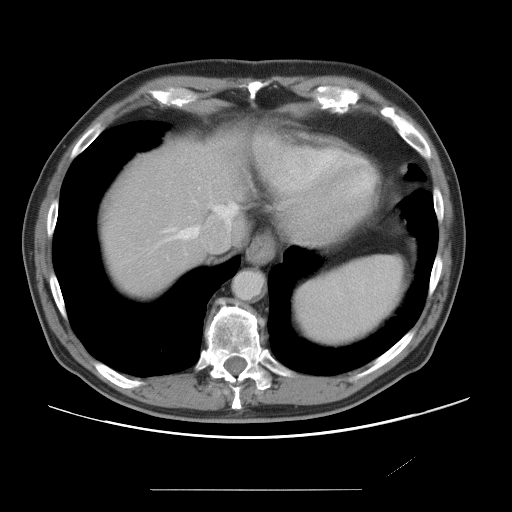
Contrast-enhanced abdominal CT, one axial slice. Slice 65 of 87 in the series (ordered by position). 120 kVp. Intravenous contrast given. Soft-tissue window (W 400 / L 40 HU). 512 × 512 image matrix, field of view 406 × 406 mm. Male patient, age 74 years. Case-level facts recorded for this patient, not image findings: diagnosis: colorectal cancer liver metastases, imaged before liver resection; multiple liver metastases: yes; largest metastasis: 1.1 cm.
Structures marked on this image (expert manual segmentation):
- hepatic veins: bounding box <167,205,222,241> (left, top, right, bottom; pixels)
- liver: <104,140,242,293>
- planned liver remnant (the part of the liver to remain after resection): <104,136,243,293>